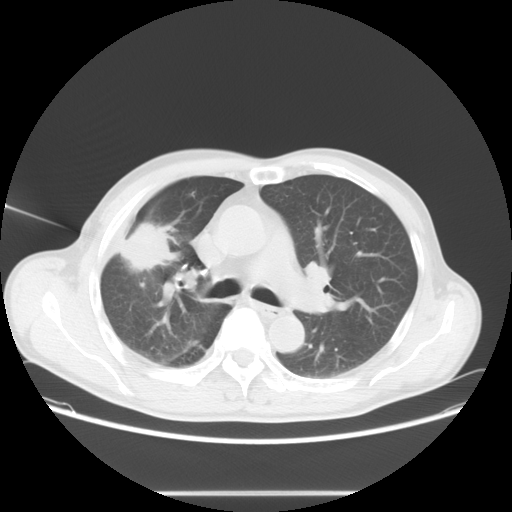
Chest CT, one axial slice; position 43 of 69 along the scan axis; lung window (W 1500 / L -600 HU); 5 mm slice thickness; 512 × 512 image matrix, field of view 392 × 392 mm. Male patient, age 67 years. Case-level facts recorded for this patient, not image findings: clinical TNM (as recorded): T2 N0 M0.
Structures marked on this image (rectangle marked by the reading radiologist):
- lung tumour (recorded histology: adenocarcinoma): bounding box <121,224,177,269> (left, top, right, bottom; pixels)